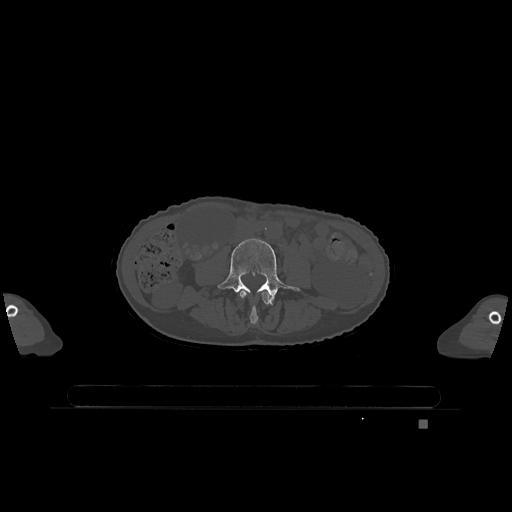
CT including the spine, one axial slice. Slice 309 of 1317 in the series (ordered by position). Bone window (W 1800 / L 400 HU). 0.5 mm slice thickness. 512 × 512 image matrix, field of view 500 × 500 mm. Patient: female, 74 years. Case-level facts recorded for this patient, not image findings: primary cancer: lung; vertebrae with lytic lesions (as recorded): T1, T4, T5, T6, L4, L5.
Outlined on this slice (semi-automatic segmentation, software-assisted and operator-edited):
- L3 vertebra: bounding box (x1, y1, x2, y2) in pixels: (239, 290, 272, 324)
- L4 vertebra: (217, 238, 300, 305)